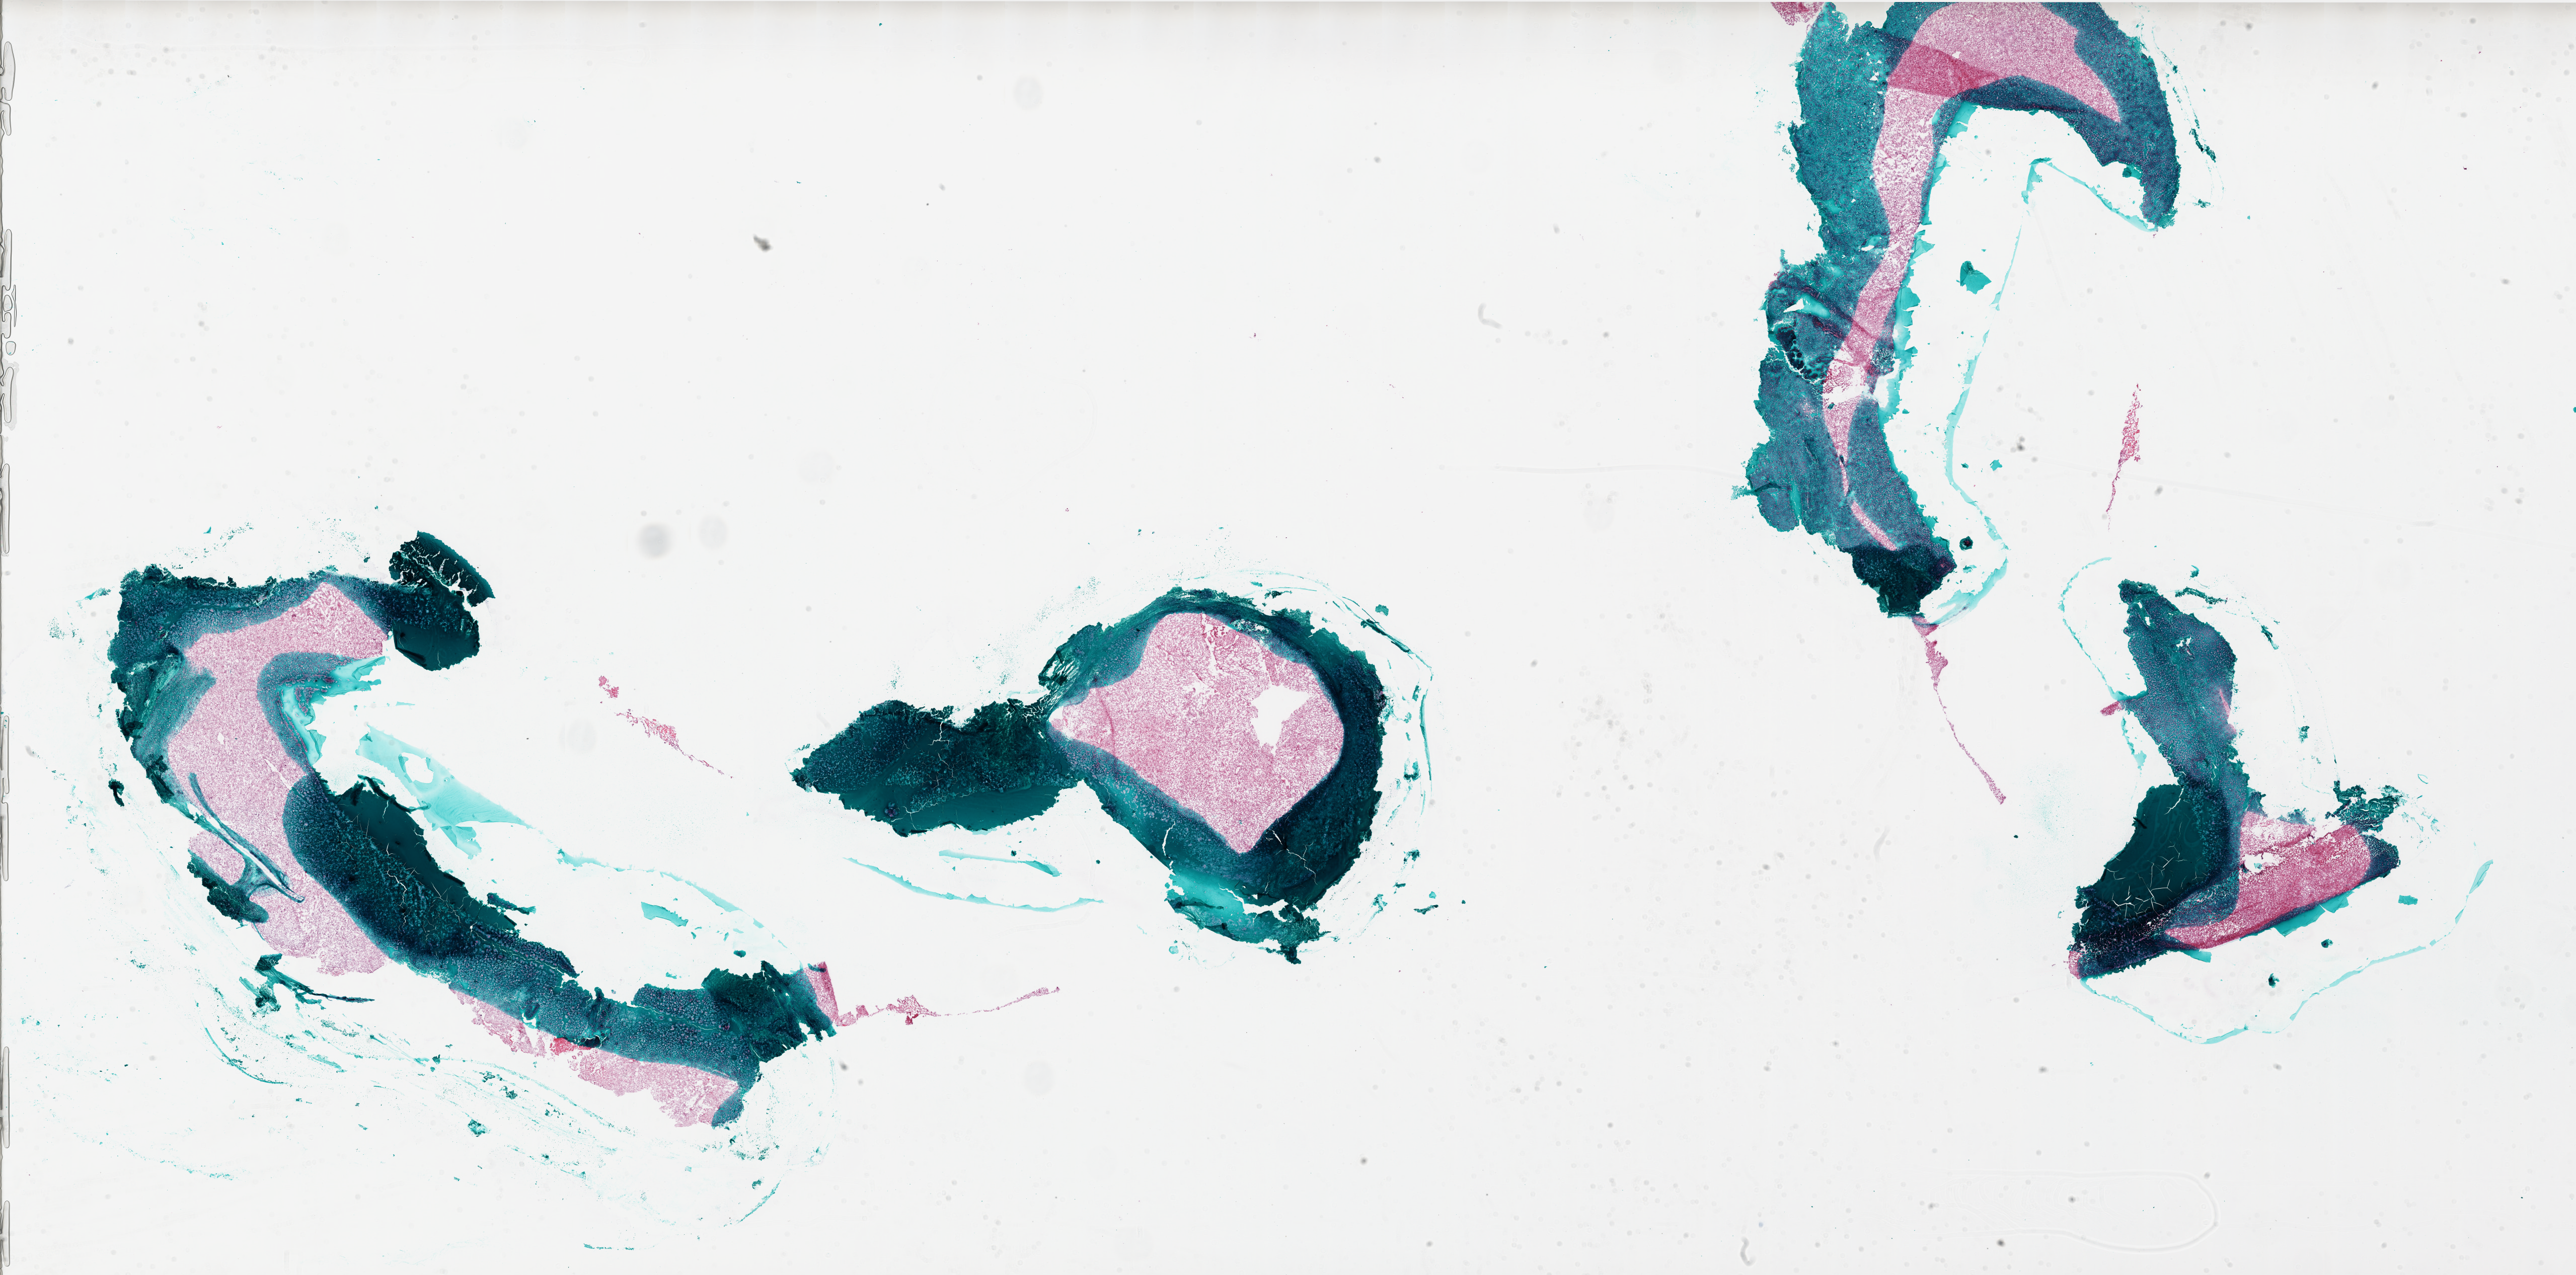
Hematoxylin and eosin (H&E) stained whole-slide image — whole scanned area (about 41.0 x 20.3 mm, from a 20x scan) shown as a low-resolution overview; frozen section from the bottom of the tissue portion; primary tumour sample from the brain. Patient: female, age at initial diagnosis 66 years.
Pathologic diagnosis: Glioblastoma.